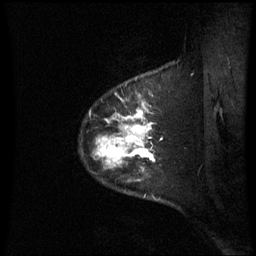
Breast MRI (dynamic contrast-enhanced), one sagittal slice; dynamic contrast-enhanced series, image 2 of 3 at this slice position (ordered by acquisition); 1.5 T; TE 4.2 ms, TR 8.9 ms; 2.4 mm slice thickness; 256 × 256 image matrix, field of view 210 × 210 mm. Female patient, age 42 years. Case-level facts recorded for this patient, not image findings: setting: breast cancer imaged before/during neoadjuvant chemotherapy; receptor status: HER2-positive.
Structures marked on this image (semi-automatically segmented with operator editing):
- analysis volume of interest (the breast-tissue region the enhancement analysis was run in; not a lesion): bounding box <91,95,164,199> (left, top, right, bottom; pixels)
- tumour enhancement mask (voxels above the 70 % enhancement threshold inside the analysis volume of interest): <96,109,155,169>